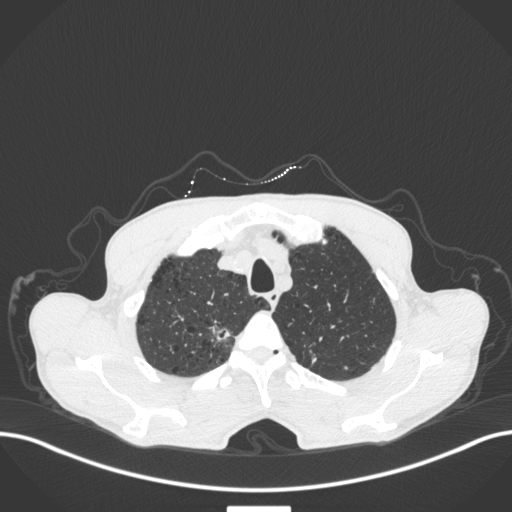
Chest CT, one axial slice; slice 366 of 445 in the series (ordered by position); 120 kVp; lung window (W 1500 / L -600 HU); 1 mm slice thickness; 512 × 512 image matrix. Patient: male, 70 years. Case-level facts recorded for this patient, not image findings: clinical TNM (as recorded): T1a N0 M0.
Outlined on this slice (rectangle marked by the reading radiologist):
- lung tumour (recorded histology: adenocarcinoma): bounding box <205,313,234,343> (left, top, right, bottom; pixels)